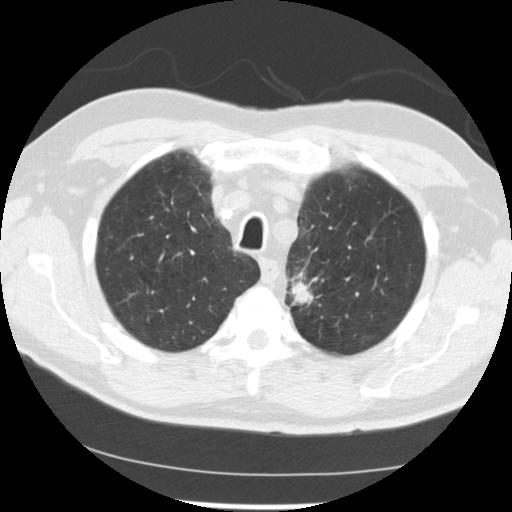
Low-dose screening chest CT, one axial slice; reconstruction kernel STANDARD; lung window (W 1500 / L -600 HU); 2.5 mm slice thickness; 512 × 512 image matrix, field of view 341 × 341 mm.
Outlined on this slice (outlined manually by an expert reader):
- lesion 2 (tumor, upper lobe of left lung): bounding box [x1, y1, x2, y2] px = [290, 280, 314, 304]